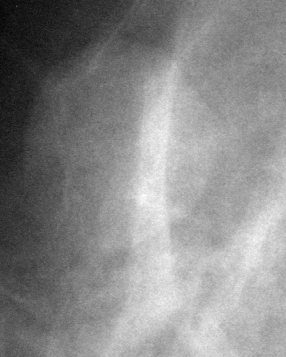
Cropped region of a digitized screen-film mammogram centred on a radiologist-marked abnormality; right breast; MLO view; BI-RADS breast density category 2 (scale 1–4).
- Mass, shape round, margins circumscribed; BI-RADS assessment category 3; subtlety rating 3 on a 1 (subtle) to 5 (obvious) scale; benign; no additional work-up was recommended (benign without callback).